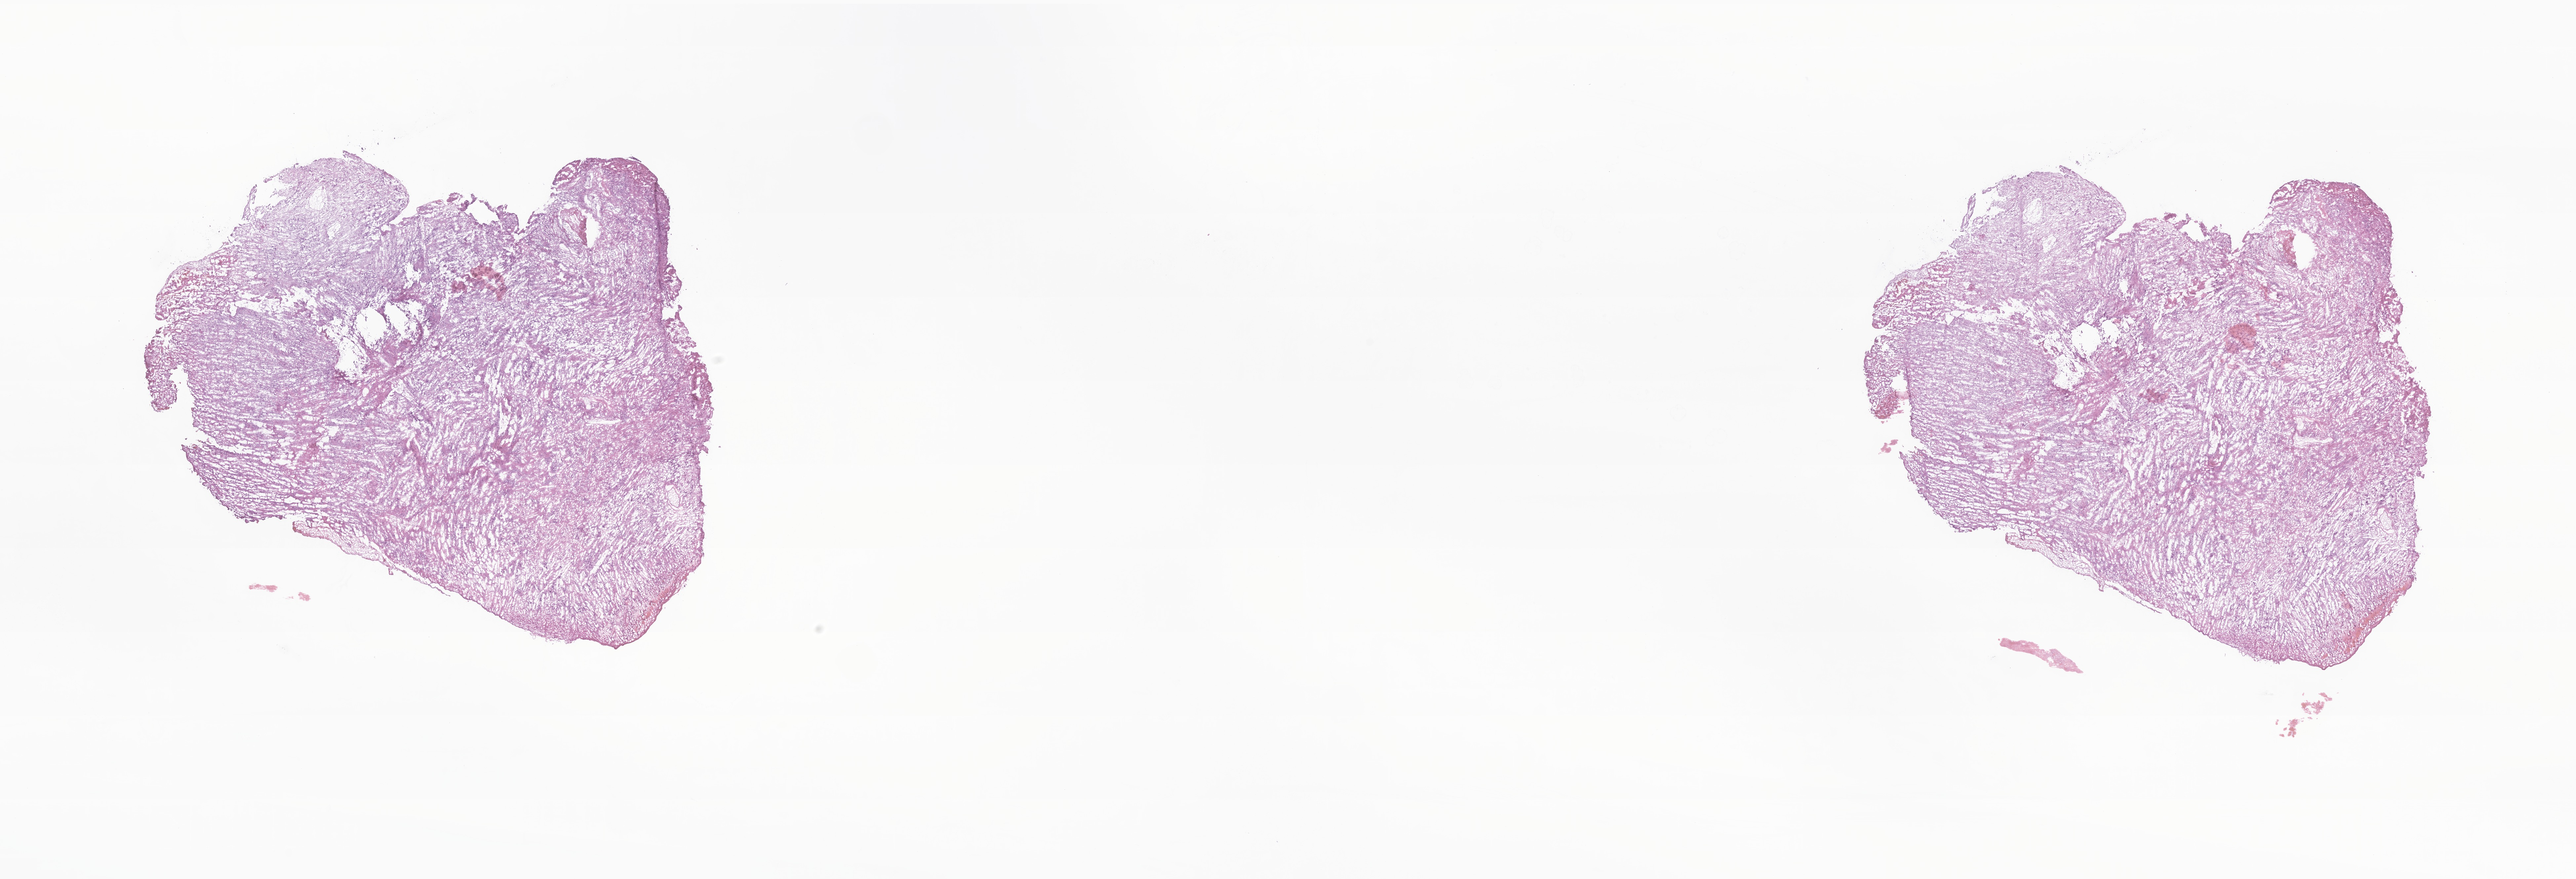
Whole-slide image, H&E stain of tumor tissue from the brain, shown as a low-resolution overview of the whole scanned area (about 32.9 x 11.2 mm); frozen section. Patient: female, age 196 months (16 years 4 months).
Diagnosis: Subependymal giant cell astrocytoma.